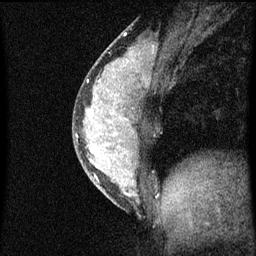
Breast MRI (dynamic contrast-enhanced), one sagittal slice. Slice 26 of 60 in the series (ordered by position). Dynamic contrast-enhanced series, image 2 of 3 at this slice position (ordered by acquisition). 1.5 T. TE 4.2 ms, TR 8 ms. 256 × 256 image matrix, field of view 180 × 180 mm. Female patient, age 33 years.
Structures marked on this image (semi-automatically segmented with operator editing):
- analysis volume of interest (the breast-tissue region the enhancement analysis was run in; not a lesion): box from (x=73, y=56) to (x=156, y=211) px
- tumour enhancement mask (voxels above the 70 % enhancement threshold inside the analysis volume of interest): (x=77, y=58)–(x=138, y=197)